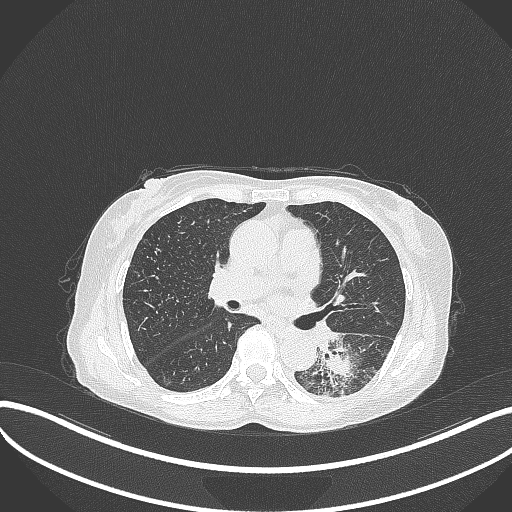
Chest CT, one axial slice; position 175 of 370 along the scan axis; lung window (W 1500 / L -600 HU); 1 mm slice thickness; 512 × 512 image matrix, field of view 400 × 400 mm. Female patient, age 78 years. Case-level facts recorded for this patient, not image findings: clinical TNM (as recorded): T3 N0 M1.
Outlined on this slice (bounding box drawn by a radiologist):
- lung tumour (recorded histology: squamous cell carcinoma): bounding box [x1, y1, x2, y2] px = [317, 329, 370, 393]